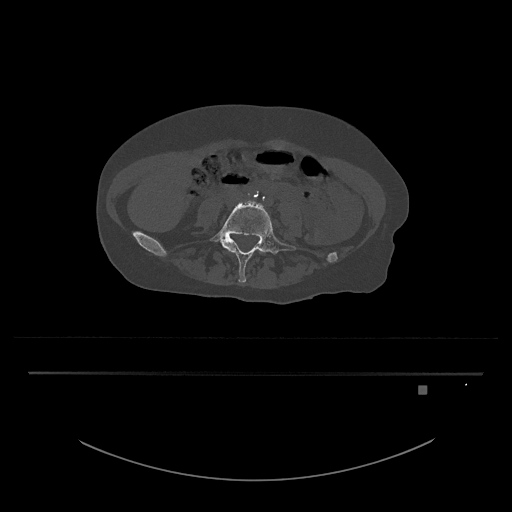
CT including the spine, one axial slice. Position 309 of 797 along the scan axis. 120 kVp. Bone window (W 1800 / L 400 HU). 0.5 mm slice thickness. 512 × 512 image matrix, field of view 500 × 500 mm. Patient: female, 57 years. From the clinical record (not read from this slice): primary cancer: cervical.
Annotated regions visible in this slice (semi-automatic segmentation, software-assisted and operator-edited):
- L4 vertebra: box from (x=259, y=252) to (x=261, y=254) px